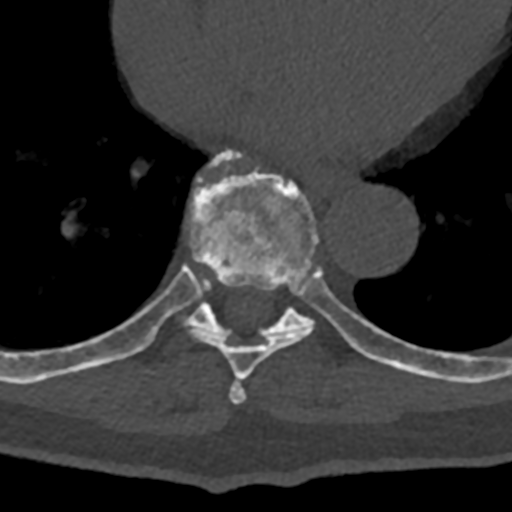
CT including the spine, one axial slice. Position 688 of 797 along the scan axis. Bone window (W 1800 / L 400 HU). 0.5 mm slice thickness. 512 × 512 image matrix, field of view 160 × 160 mm. Patient: male, 74 years. From the clinical record (not read from this slice): primary cancer: renal; vertebrae with lytic lesions (as recorded): T10, L1, L2, L3, L4, L5.
Outlined on this slice (semi-automatic segmentation, software-assisted and operator-edited):
- T7 vertebra: bounding box (x1, y1, x2, y2) in pixels: (229, 378, 247, 404)
- T8 vertebra: (70, 153, 383, 379)
- T9 vertebra: (104, 149, 432, 378)